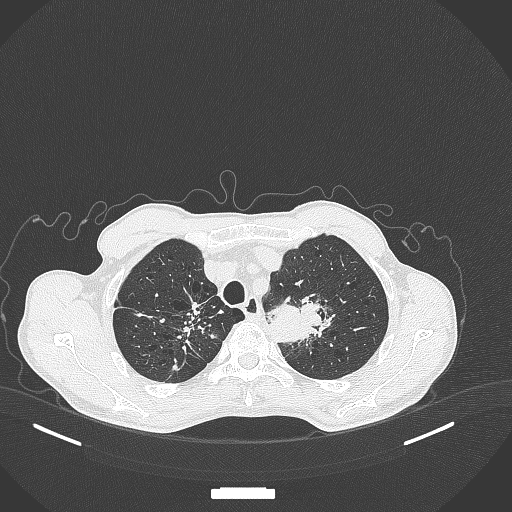
Chest CT, one axial slice. Slice 355 of 386 in the series (ordered by position). Reconstruction kernel B70f. 120 kVp. Lung window (W 1500 / L -600 HU). 512 × 512 image matrix, field of view 400 × 400 mm. Male patient, age 65 years. Case-level facts recorded for this patient, not image findings: clinical TNM (as recorded): T2b N0 M0.
Outlined on this slice (bounding box drawn by a radiologist):
- lung tumour (recorded histology: adenocarcinoma): bounding box [x1, y1, x2, y2] px = [268, 290, 338, 347]